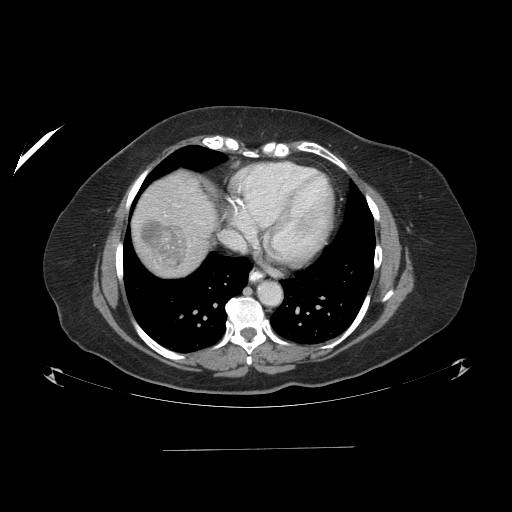
Contrast-enhanced abdominal CT (liver protocol), one axial slice; position 82 of 103 along the scan axis; 120 kVp; one of 2 acquisitions stored at this slice position; soft-tissue window (W 400 / L 40 HU); 2.5 mm slice thickness; 512 × 512 image matrix, field of view 500 × 500 mm. Case-level facts recorded for this patient, not image findings: diagnosis: hepatocellular carcinoma (patient treated with transarterial chemoembolisation; whether this scan precedes or follows treatment is not stated here); TNM stage (as recorded): Stage-IIIA; Child-Pugh class: A; tumour nodularity: multinodular; tumour size: 5.2 cm.
Outlined on this slice (semi-automatically segmented with operator editing):
- liver parenchyma outside the tumour (the mass and vessels are separate outlines, so this box may not span the whole liver): bounding box [x1, y1, x2, y2] px = [132, 170, 214, 276]
- mass: [139, 219, 188, 268]